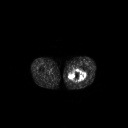
FDG PET of an extremity soft-tissue mass (from a PET/CT study), one axial slice; slice 245 of 267 in the series (ordered by position); 3.27 mm slice thickness; 128 × 128 image matrix, field of view 700 × 700 mm. Patient: male, 44 years. Case-level facts recorded for this patient, not image findings: histological type: undifferentiated pleomorphic liposarcoma; grade: high; site of the primary tumour: left thigh.
Outlined on this slice (expert contour drawn on MRI and transferred to this co-registered scan by the dataset authors):
- gross tumour volume including surrounding oedema: box from (x=67, y=69) to (x=86, y=83) px
- gross tumour volume (mass): (x=69, y=69)–(x=86, y=81)